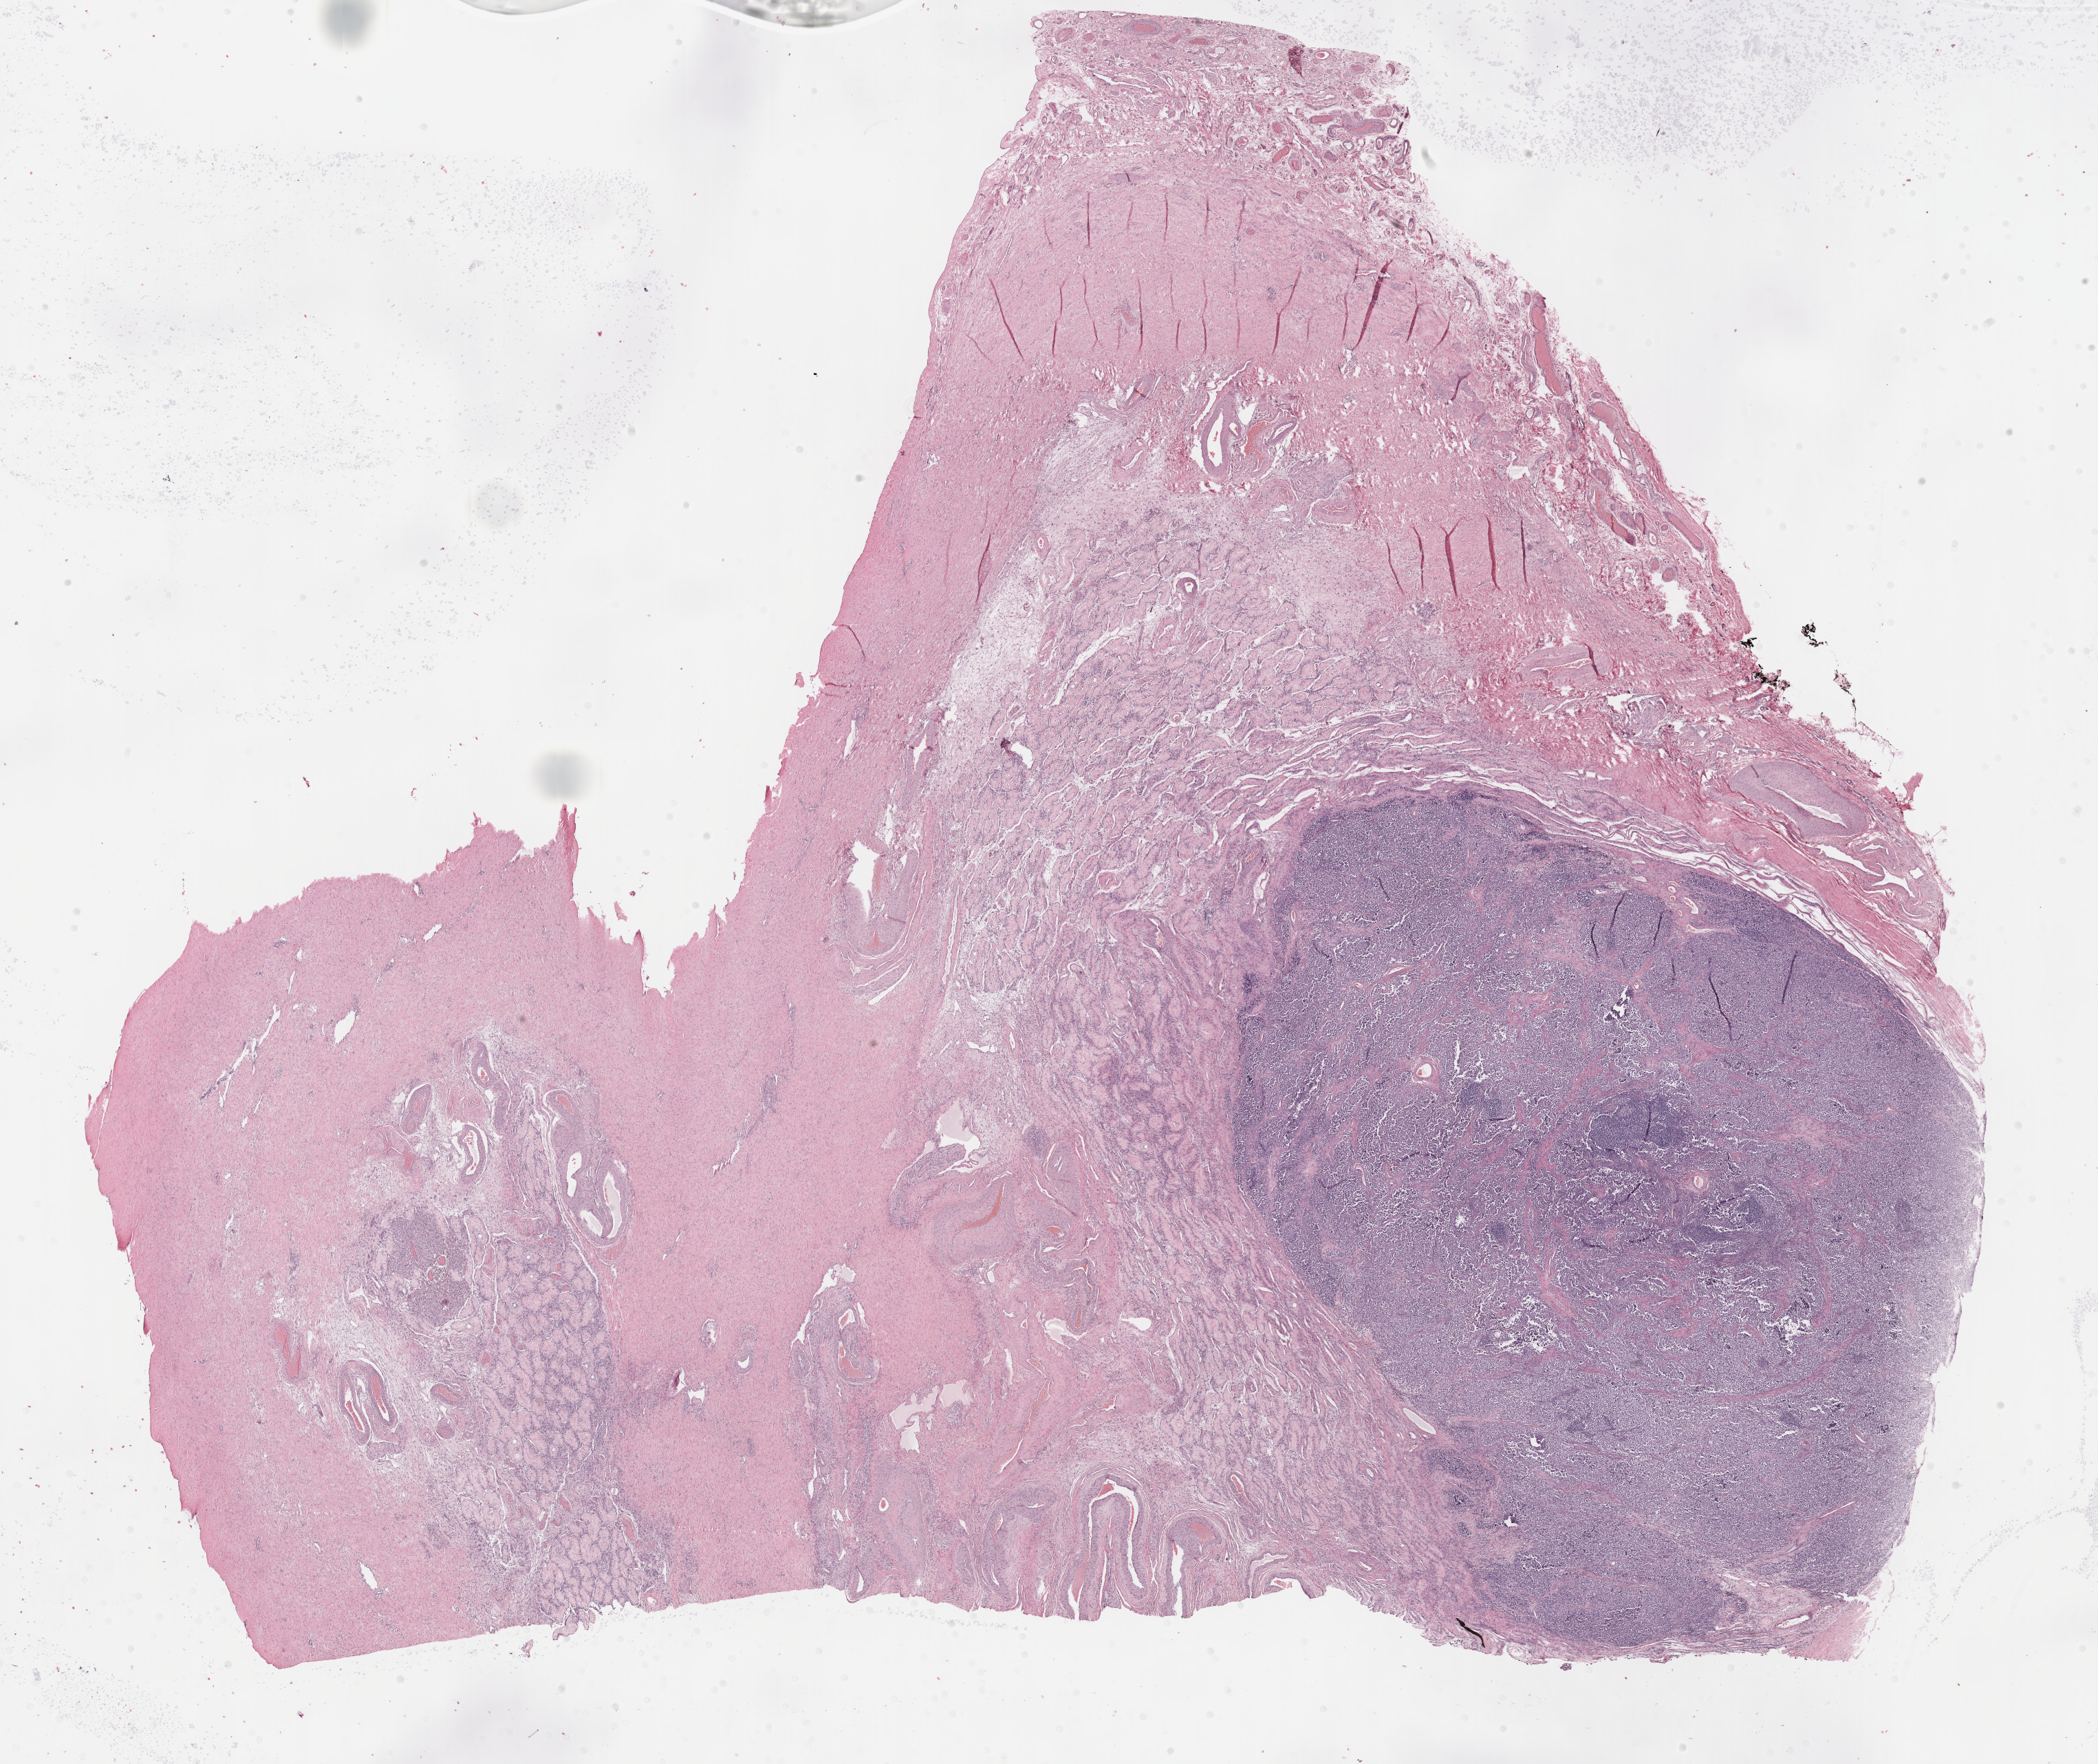
Hematoxylin and eosin (H&E) stained whole-slide image — shown as a low-resolution overview of the whole scanned area (about 24.7 x 20.7 mm); FFPE section; testis, primary tumour sample. Patient: male, age at initial diagnosis 31 years.
Pathologic diagnosis: Seminoma, NOS. Laterality: right. AJCC pathologic stage: IA (7th edition).